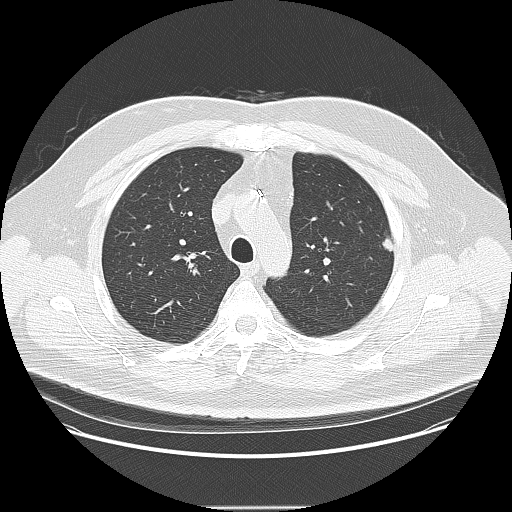
Low-dose screening chest CT, one axial slice. Position 112 of 157 along the scan axis. Reconstruction kernel LUNG. Lung window (W 1500 / L -600 HU). 2.5 mm slice thickness. 512 × 512 image matrix.
Annotated regions visible in this slice (expert manual segmentation):
- lesion 1 (tumor, upper lobe of left lung): bounding box [x1, y1, x2, y2] px = [382, 238, 393, 252]